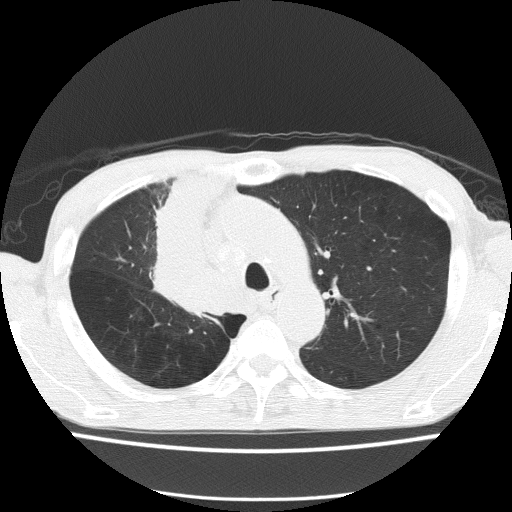
Chest CT (low-dose screening protocol), one axial image. Baseline annual screen. Lung window (W 1500 / L -600 HU). 2 mm slice thickness. Lung (sharp) reconstruction kernel (FC51). Slice 43 of 150 in the series. 512 × 512 image matrix, field of view 336 × 336 mm. Male participant, aged 59 years at enrolment.
Expert-annotated lung lesion, bounding box [x1, y1, x2, y2] px = [135, 233, 237, 325]. The screening reader recorded 5 non-calcified nodules or masses ≥4 mm on this exam (left upper lobe, left upper lobe, left upper lobe, right middle lobe, right lower lobe); which of them this box marks is not recorded. Later outcome: lung cancer diagnosed 72 days after this screen — squamous cell carcinoma, NOS, right upper lobe, moderately differentiated (G2), stage IV (AJCC 6th edition).